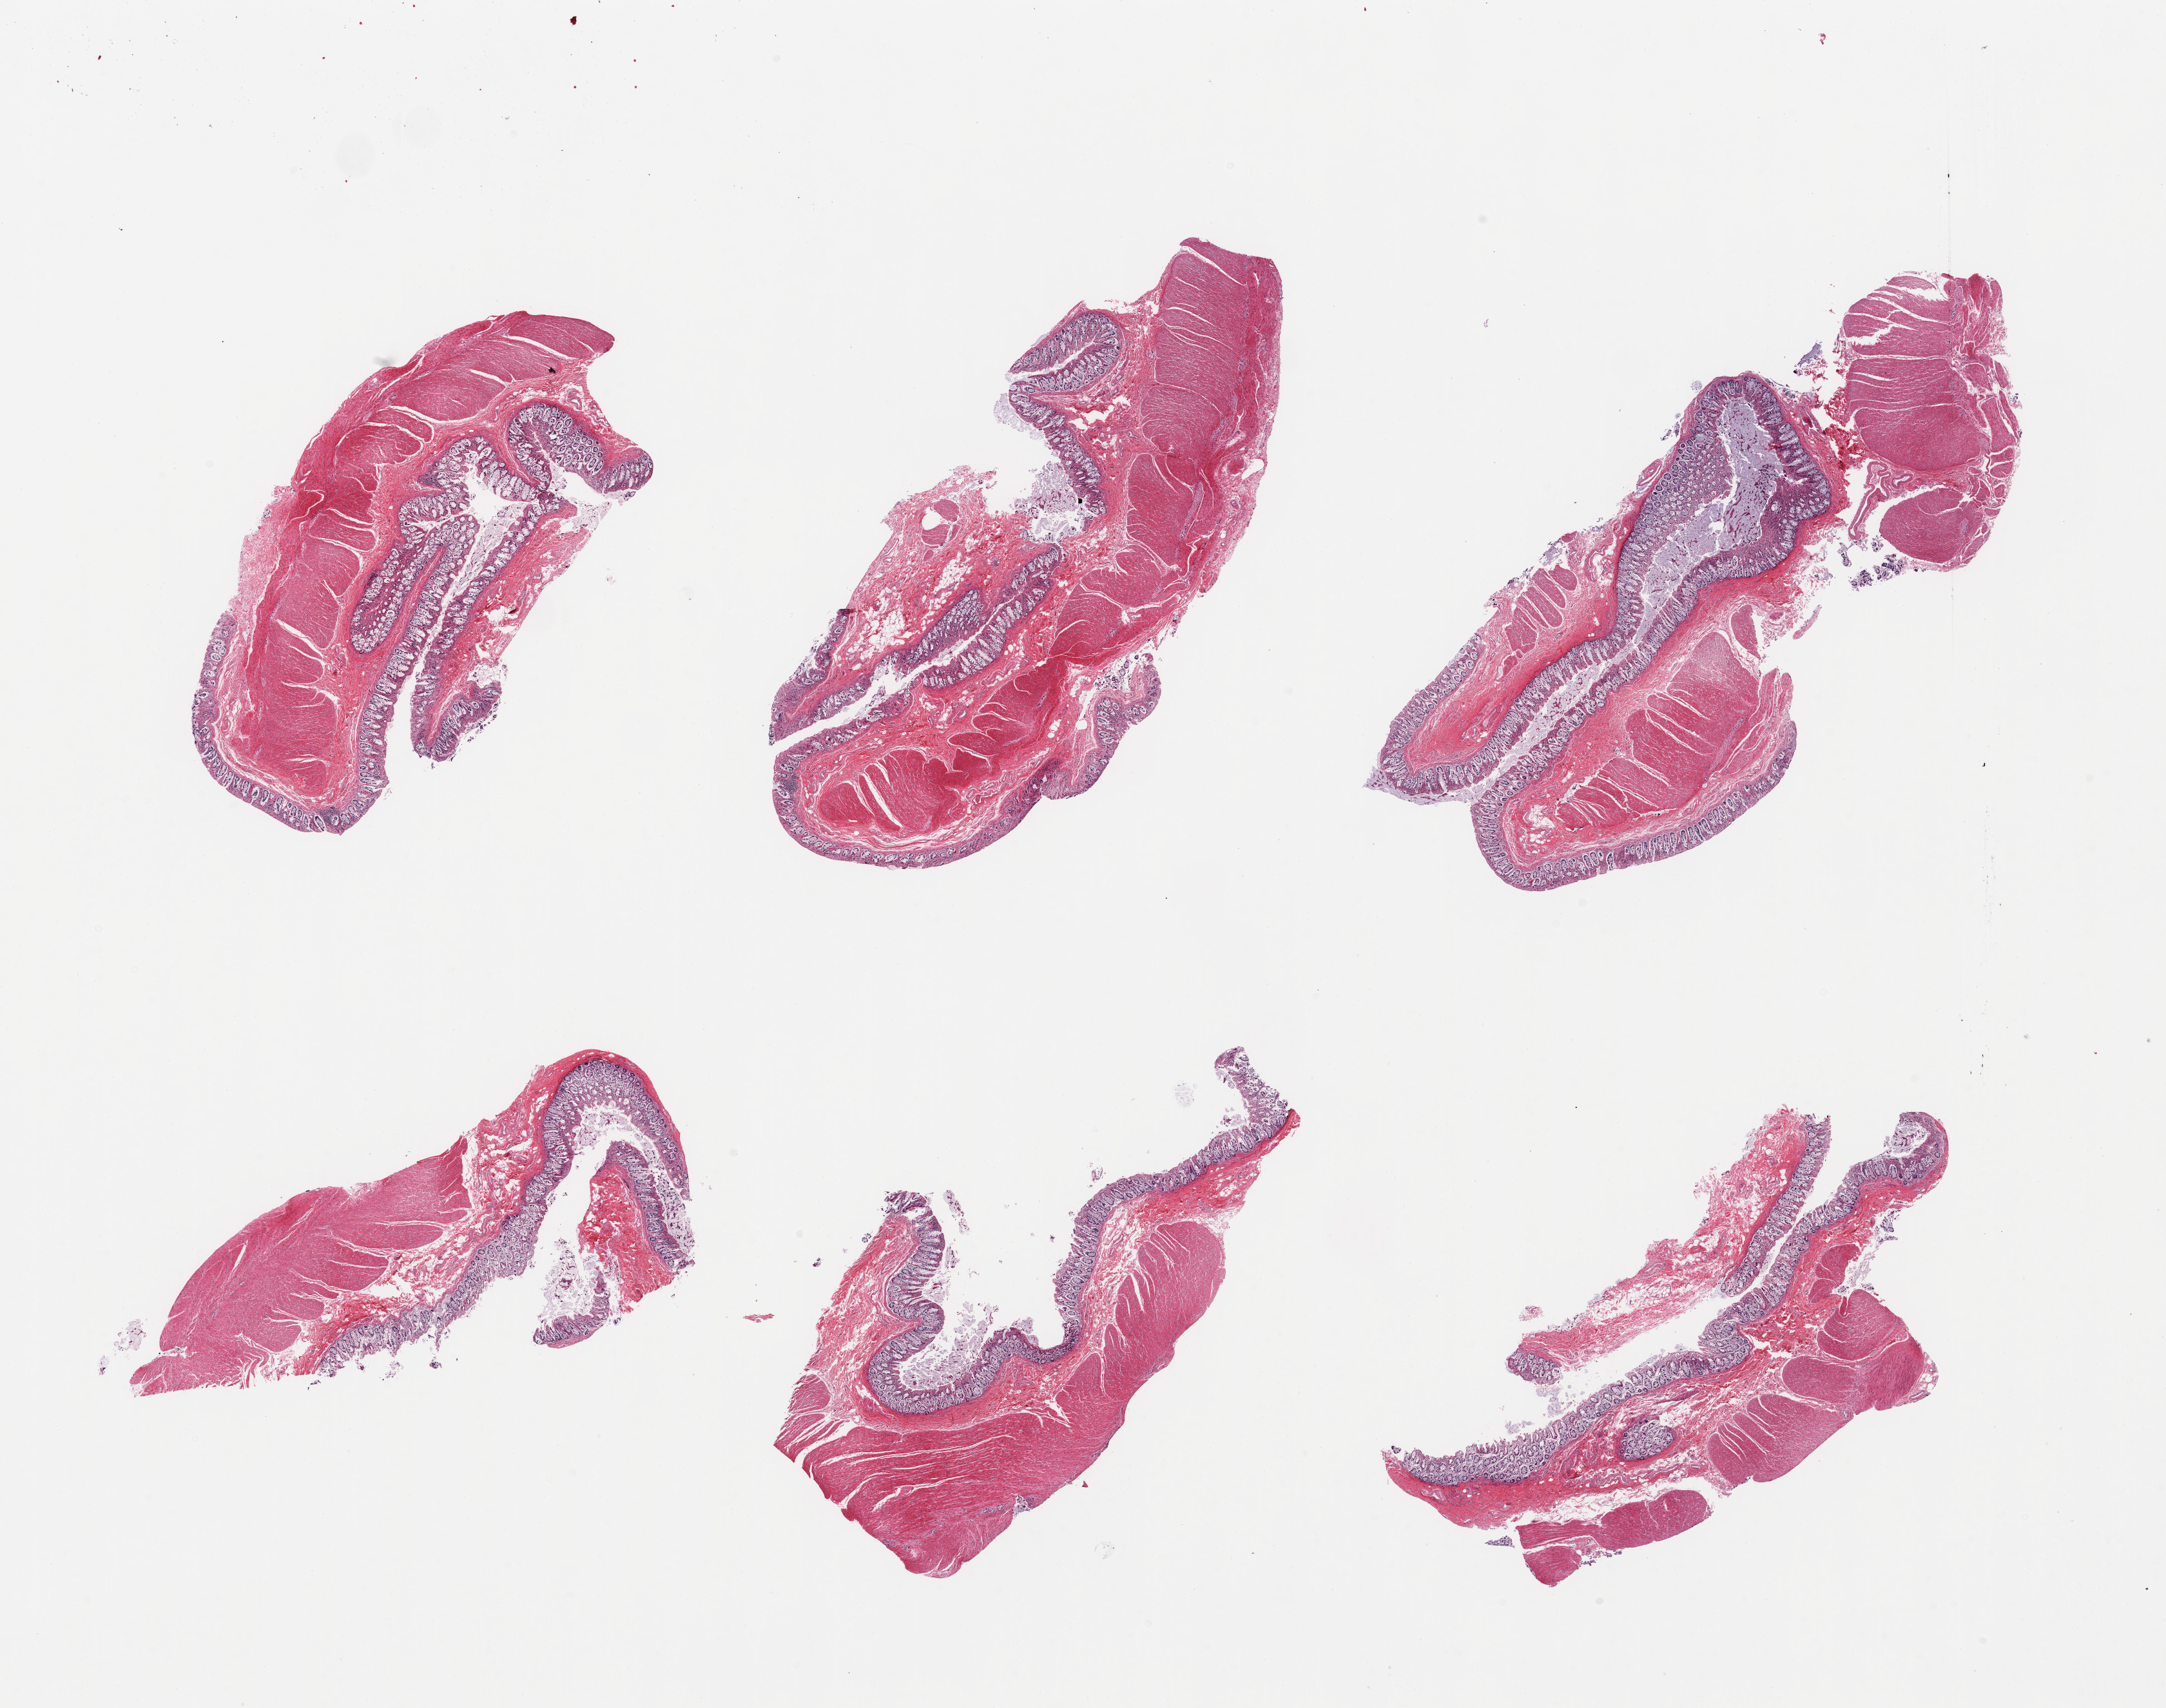
H&E whole-slide image — low-resolution overview of the scanned area, about 26.6 x 21.0 mm. PAXgene-fixed, paraffin-embedded tissue. Sampled site (target tissue): sigmoid colon. Tissue donor sample. Male donor.
Review note (as recorded): 6 pieces, target muscularis present, ~20% autolyzed mucosa.